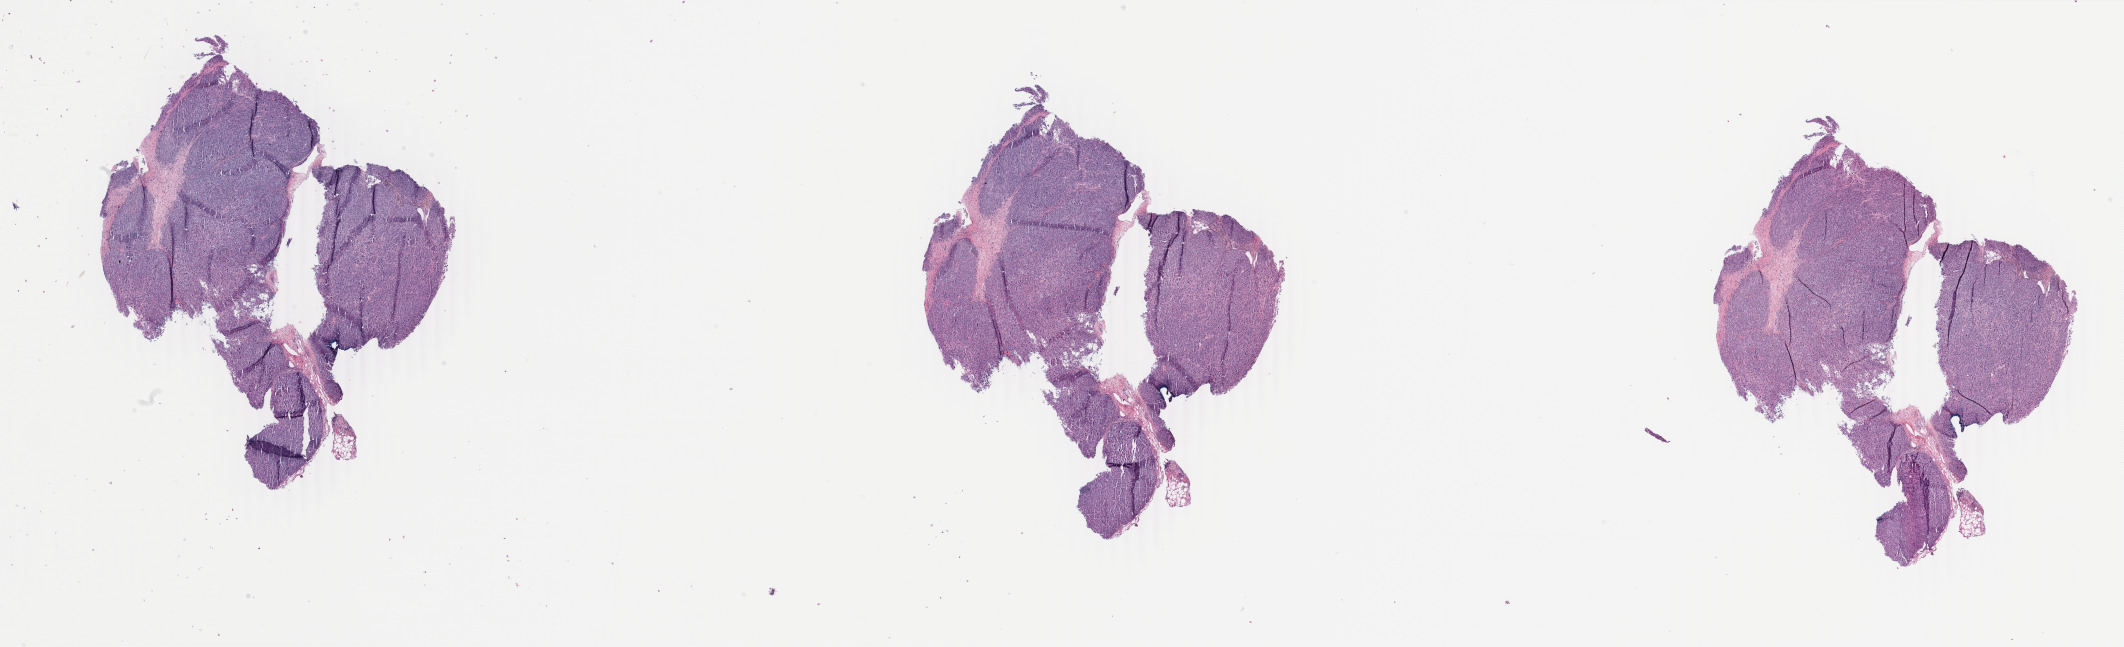
Whole-slide histology image, H&E — shown as a low-resolution overview of the whole scanned area (about 33.8 x 10.3 mm), FFPE section, skin, primary tumour sample. Patient: male, age at initial diagnosis 52 years.
AJCC pathologic stage: IIIB (7th edition). Pathologic diagnosis: Malignant melanoma, NOS.